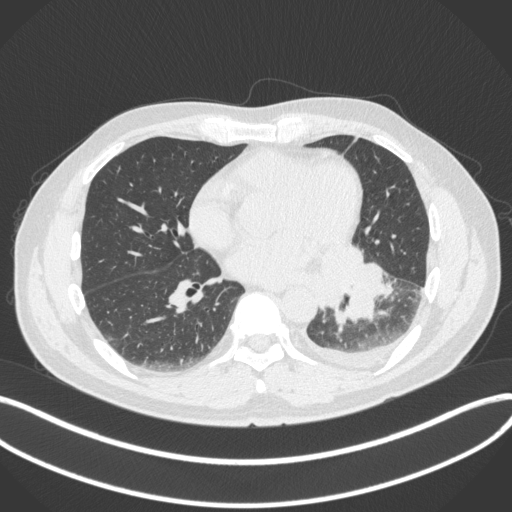
Chest CT, one axial slice. Slice 157 of 350 in the series (ordered by position). Reconstruction kernel B31f. 120 kVp. Lung window (W 1500 / L -600 HU). 1 mm slice thickness. 512 × 512 image matrix, field of view 400 × 400 mm. Patient: male, 58 years. Case-level facts recorded for this patient, not image findings: clinical TNM (as recorded): T3 N1 M1b; histopathological grade: G3.
Annotated regions visible in this slice (bounding box drawn by a radiologist):
- lung tumour (recorded histology: small cell carcinoma): bounding box <318,243,395,331> (left, top, right, bottom; pixels)